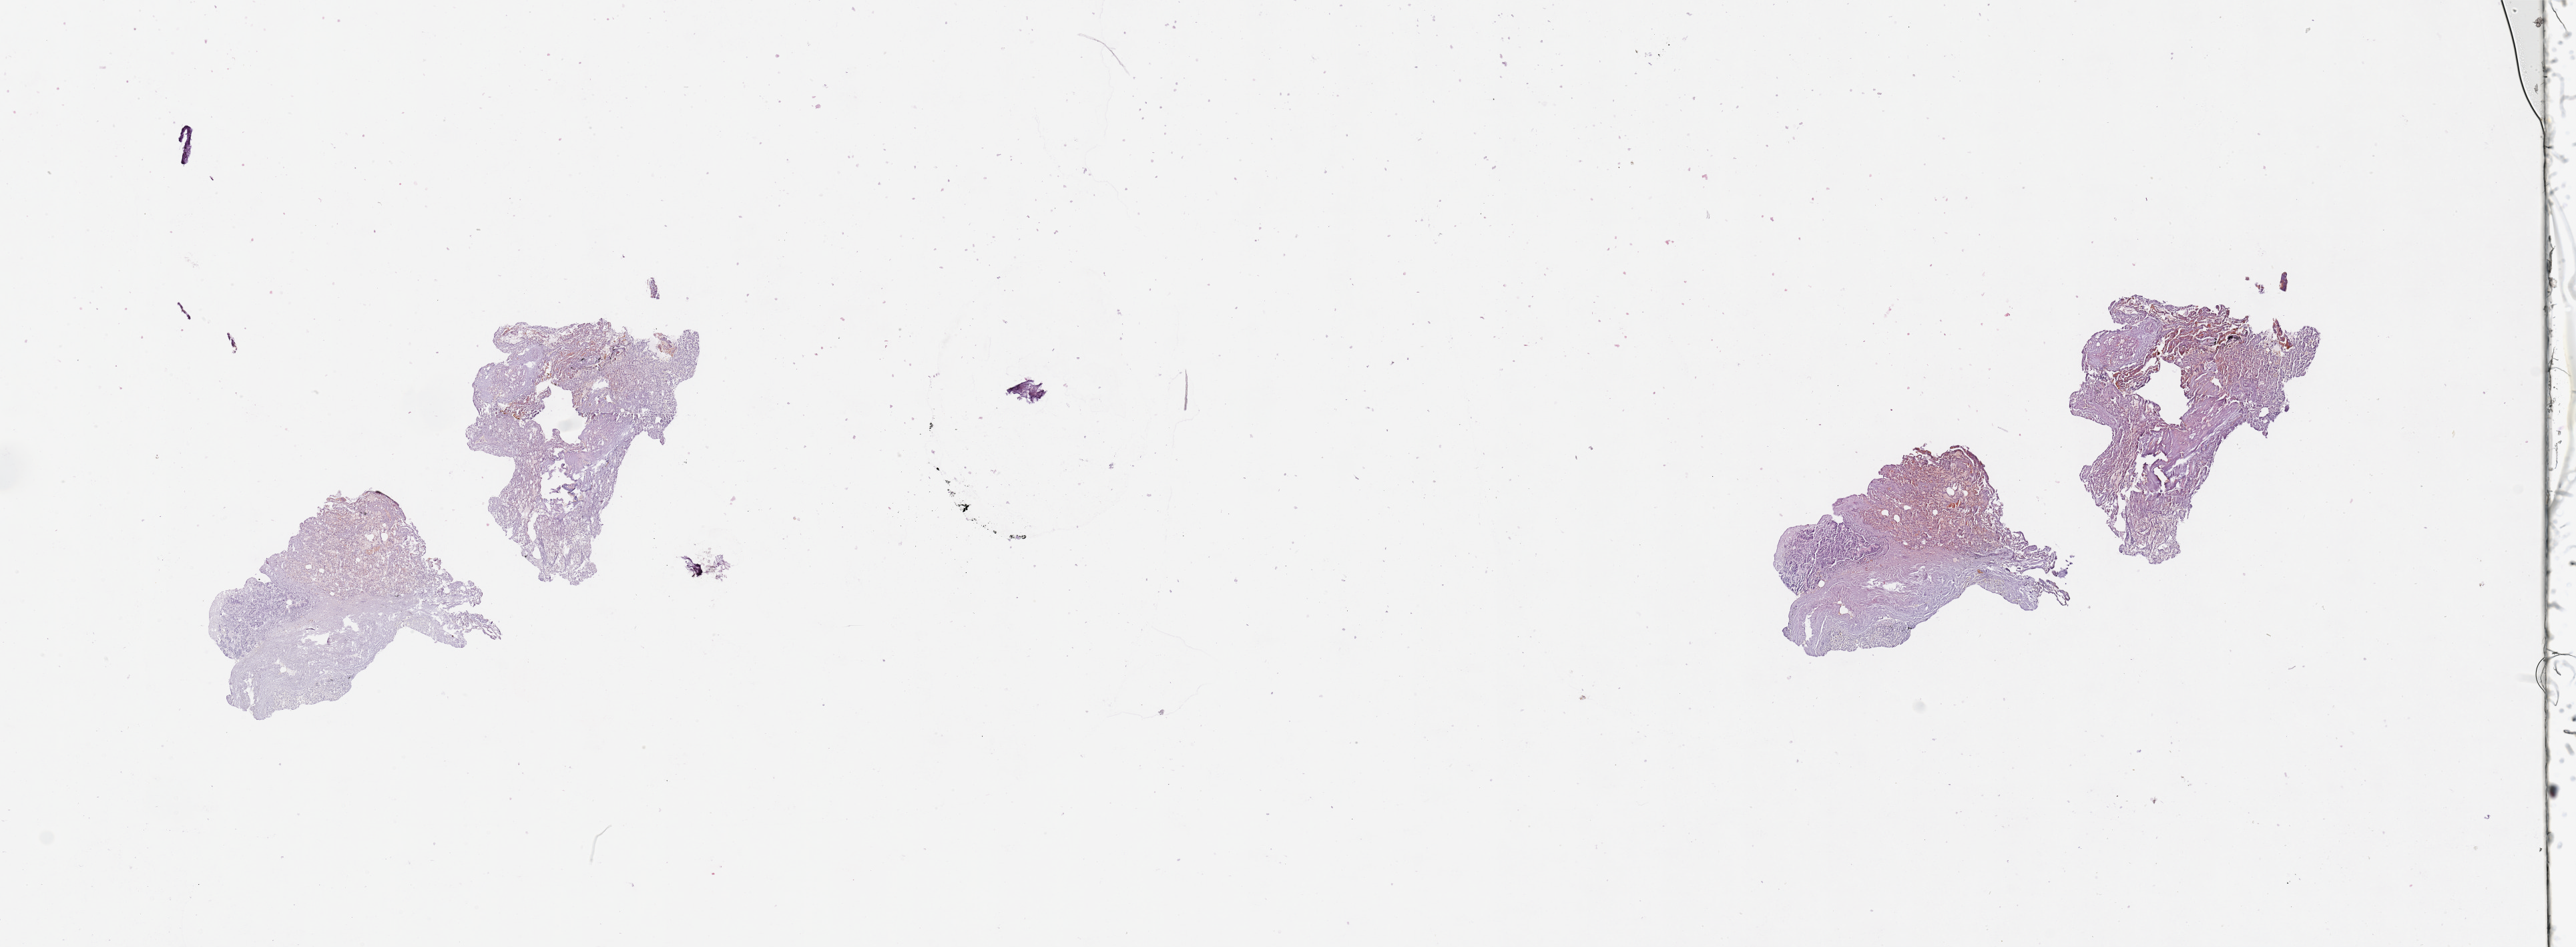
Digitized H&E-stained tissue section (whole slide), low-resolution overview of the scanned area, about 30.5 x 11.2 mm (from a 20x scan); lung, normal (non-tumour) tissue. Male, 74 y/o.
This section: normal (non-tumour) tissue from the same patient. Patient diagnosis: Squamous cell carcinoma, NOS.